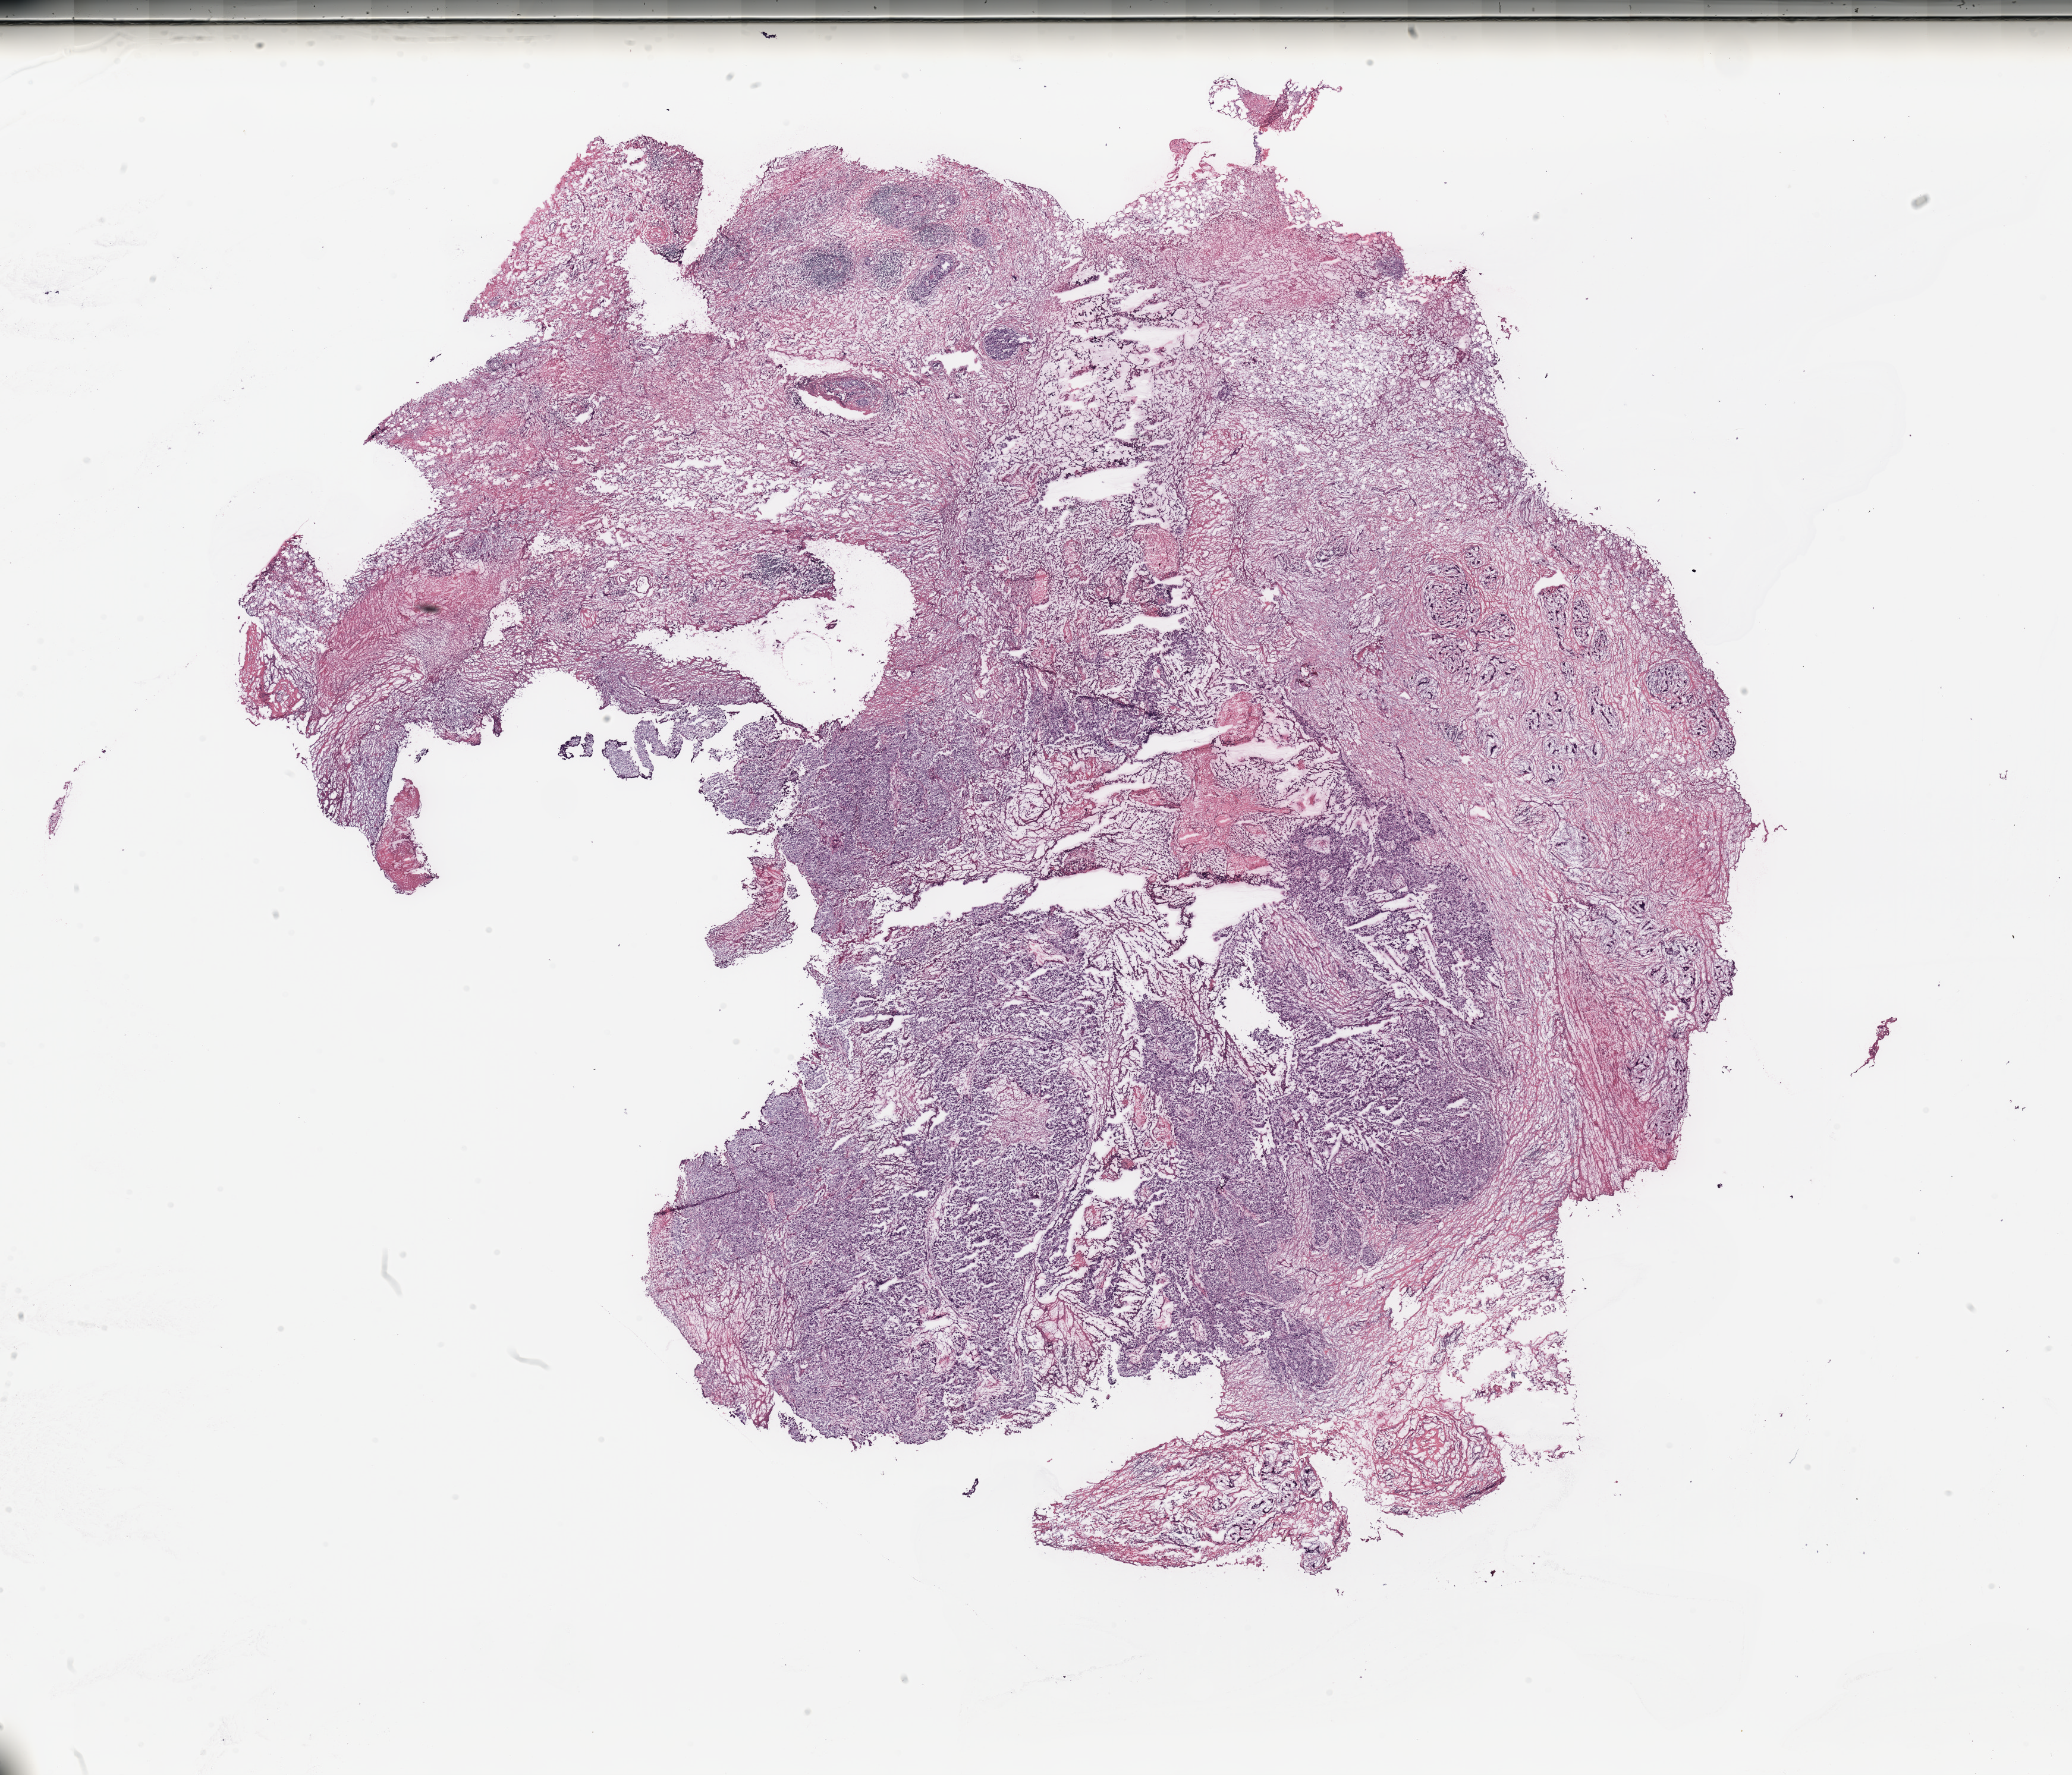
H&E whole-slide image — shown as a low-resolution overview of the whole scanned area (about 27.6 x 23.6 mm, from a 20x scan), breast, tissue type not recorded.
Patient diagnosis (cohort enrolment): breast cancer (breast).